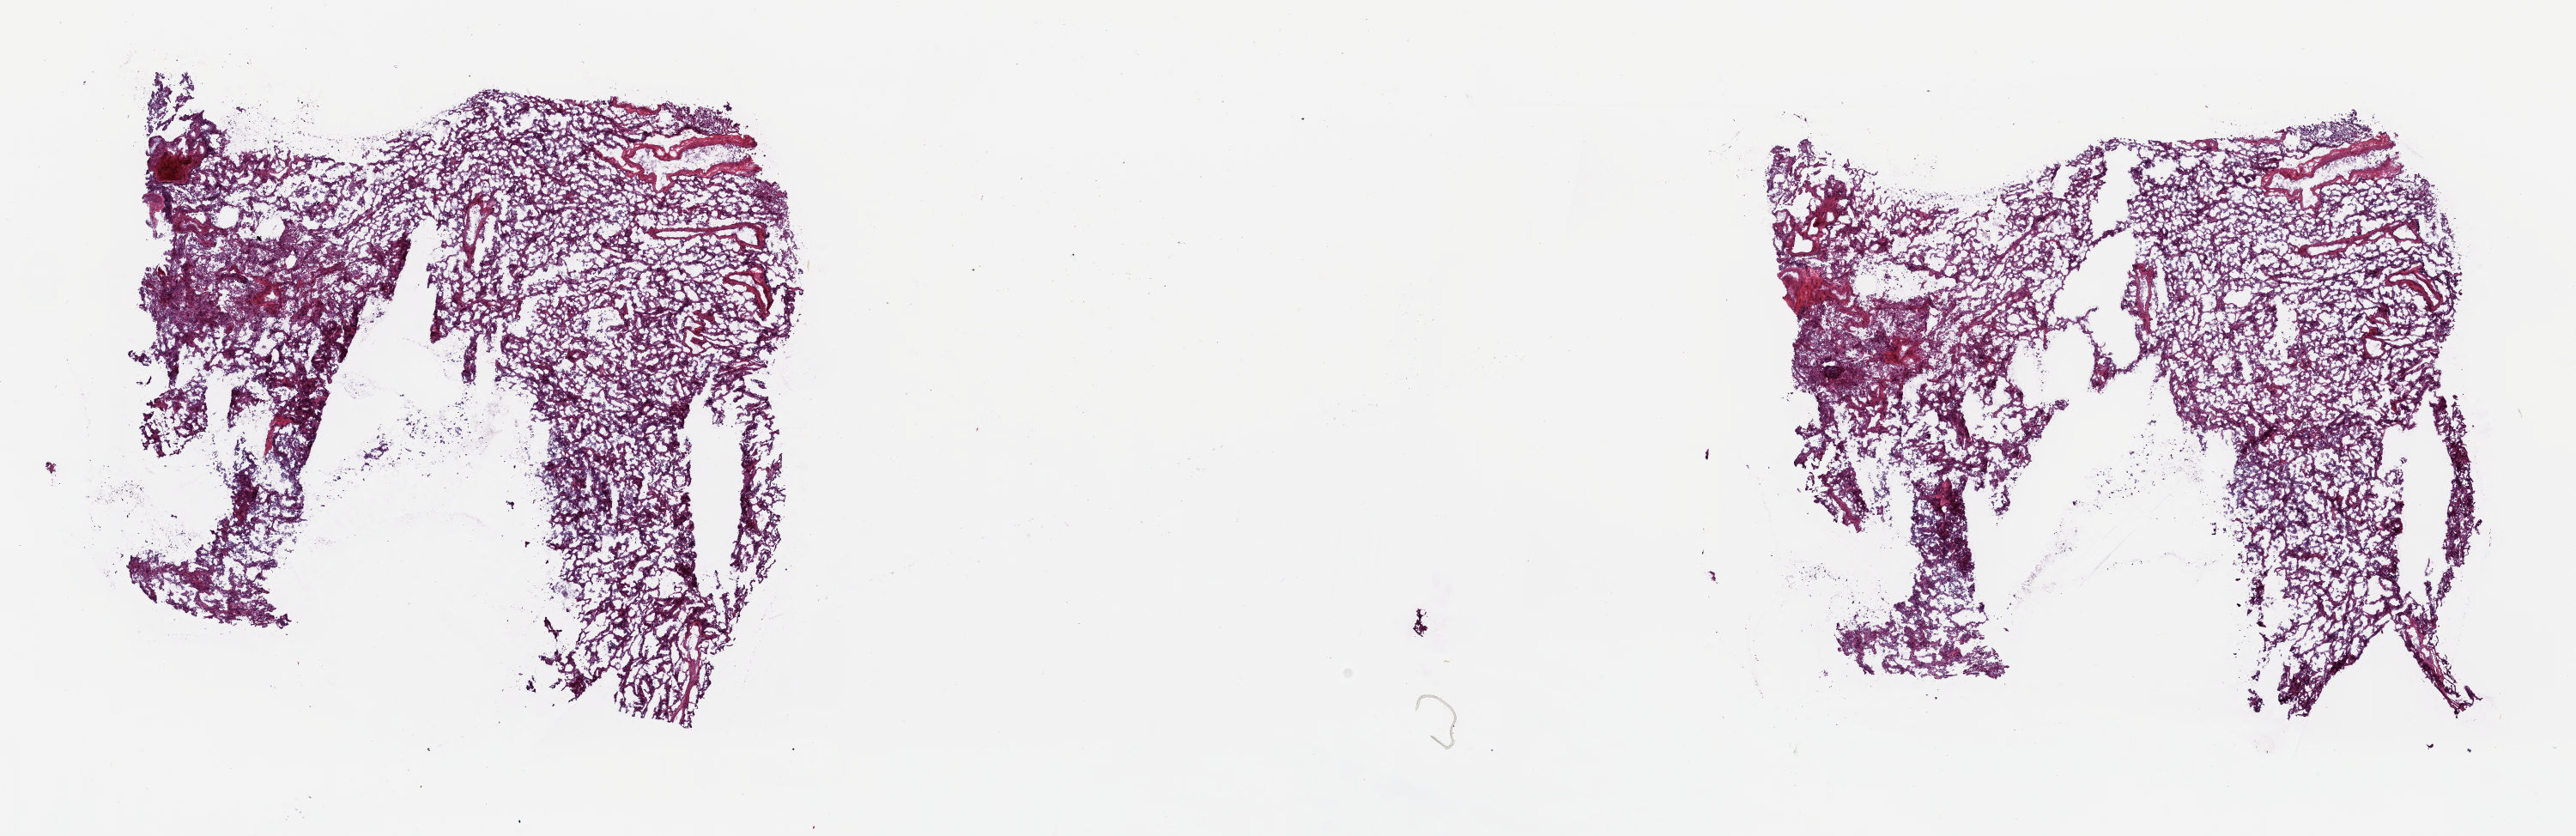
Whole-slide histology image, Hematoxylin and eosin (H&E) stained — low-resolution overview of the scanned area, about 23.8 x 7.7 mm; frozen section from the top of the tissue portion; solid tissue normal (non-tumour tissue) sample from the lung. Patient: female, age at initial diagnosis 63 years. Pathologist review of this section (percent, as recorded): tumour cells 0%, tumour nuclei 0%, normal cells 100%, stromal cells 0%, necrosis 0%. Infiltration values recorded for this section: lymphocyte infiltration 0%, monocyte infiltration 0%, neutrophil infiltration 0%.
This section: solid tissue normal (non-tumour) sample from the same patient. Patient diagnosis: Adenocarcinoma with mixed subtypes (lower lobe, lung).